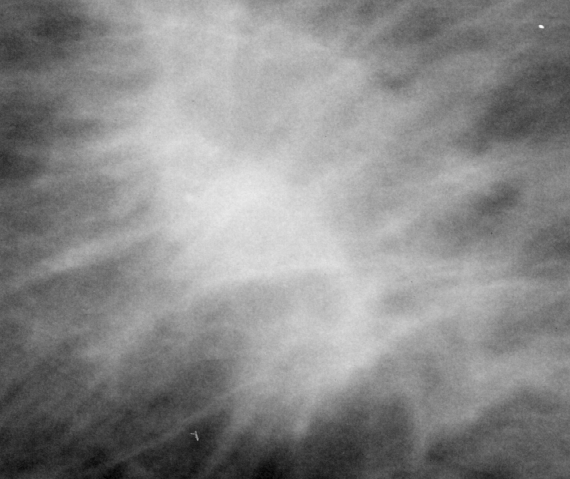
Region of interest cut from a scanned film mammogram (one marked finding), right breast, MLO view.
Marked abnormality: mass, shape irregular / architectural distortion, margins spiculated; BI-RADS assessment category 5; subtlety rating 5 on a 1 (subtle) to 5 (obvious) scale; pathology result (as recorded, not read from the image): malignant.